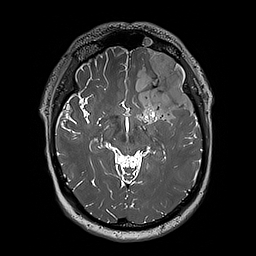
Brain MRI from a brain-tumour surgery series, one axial slice; position 121 of 192 along the scan axis; 1 mm slice thickness; 256 × 256 image matrix, field of view 250 × 250 mm. From the clinical record (not read from this slice): histopathology: Oligodendroglioma; WHO grade: 3; IDH mutation: yes.
Annotated regions visible in this slice (manually delineated by an expert):
- tumour: bounding box <124,51,197,124> (left, top, right, bottom; pixels)